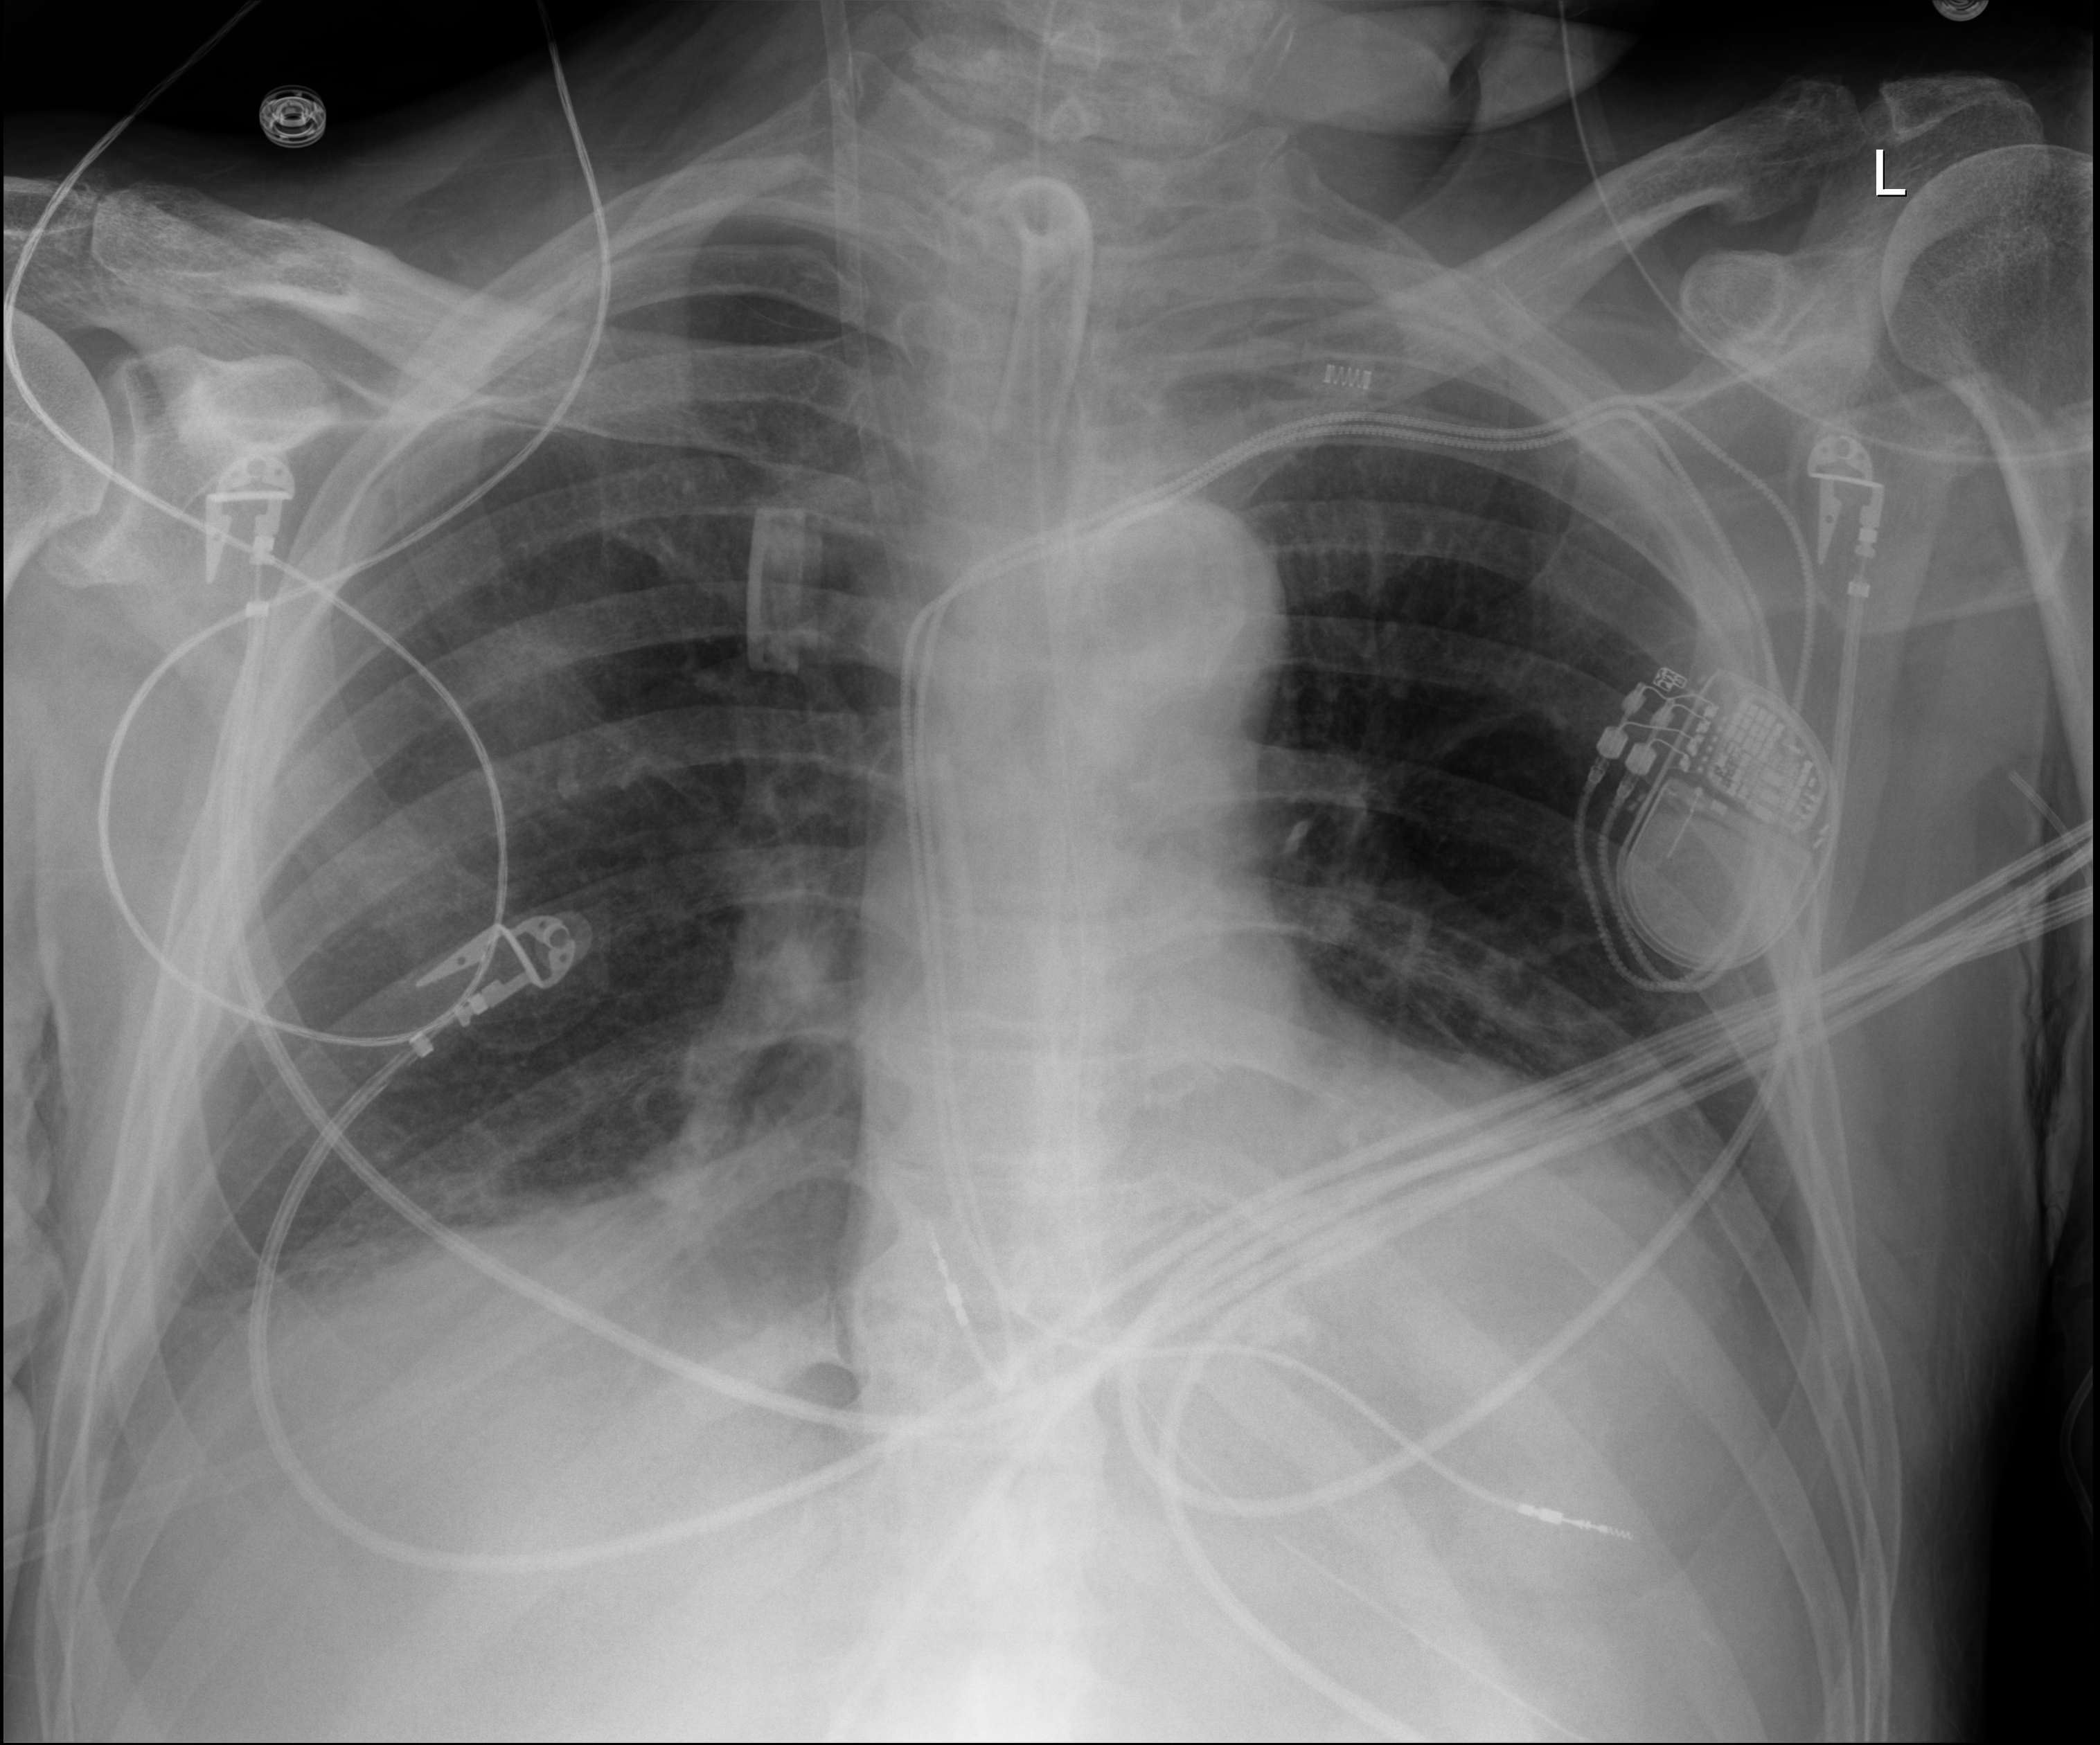
Chest X-ray (portable); anteroposterior (AP) projection. Patient hospitalised with COVID-19; male, aged 60–74 years.
Admission-level facts for this patient (not findings on this image; timing relative to this image not recorded):
- mechanically ventilated during this hospital stay: yes